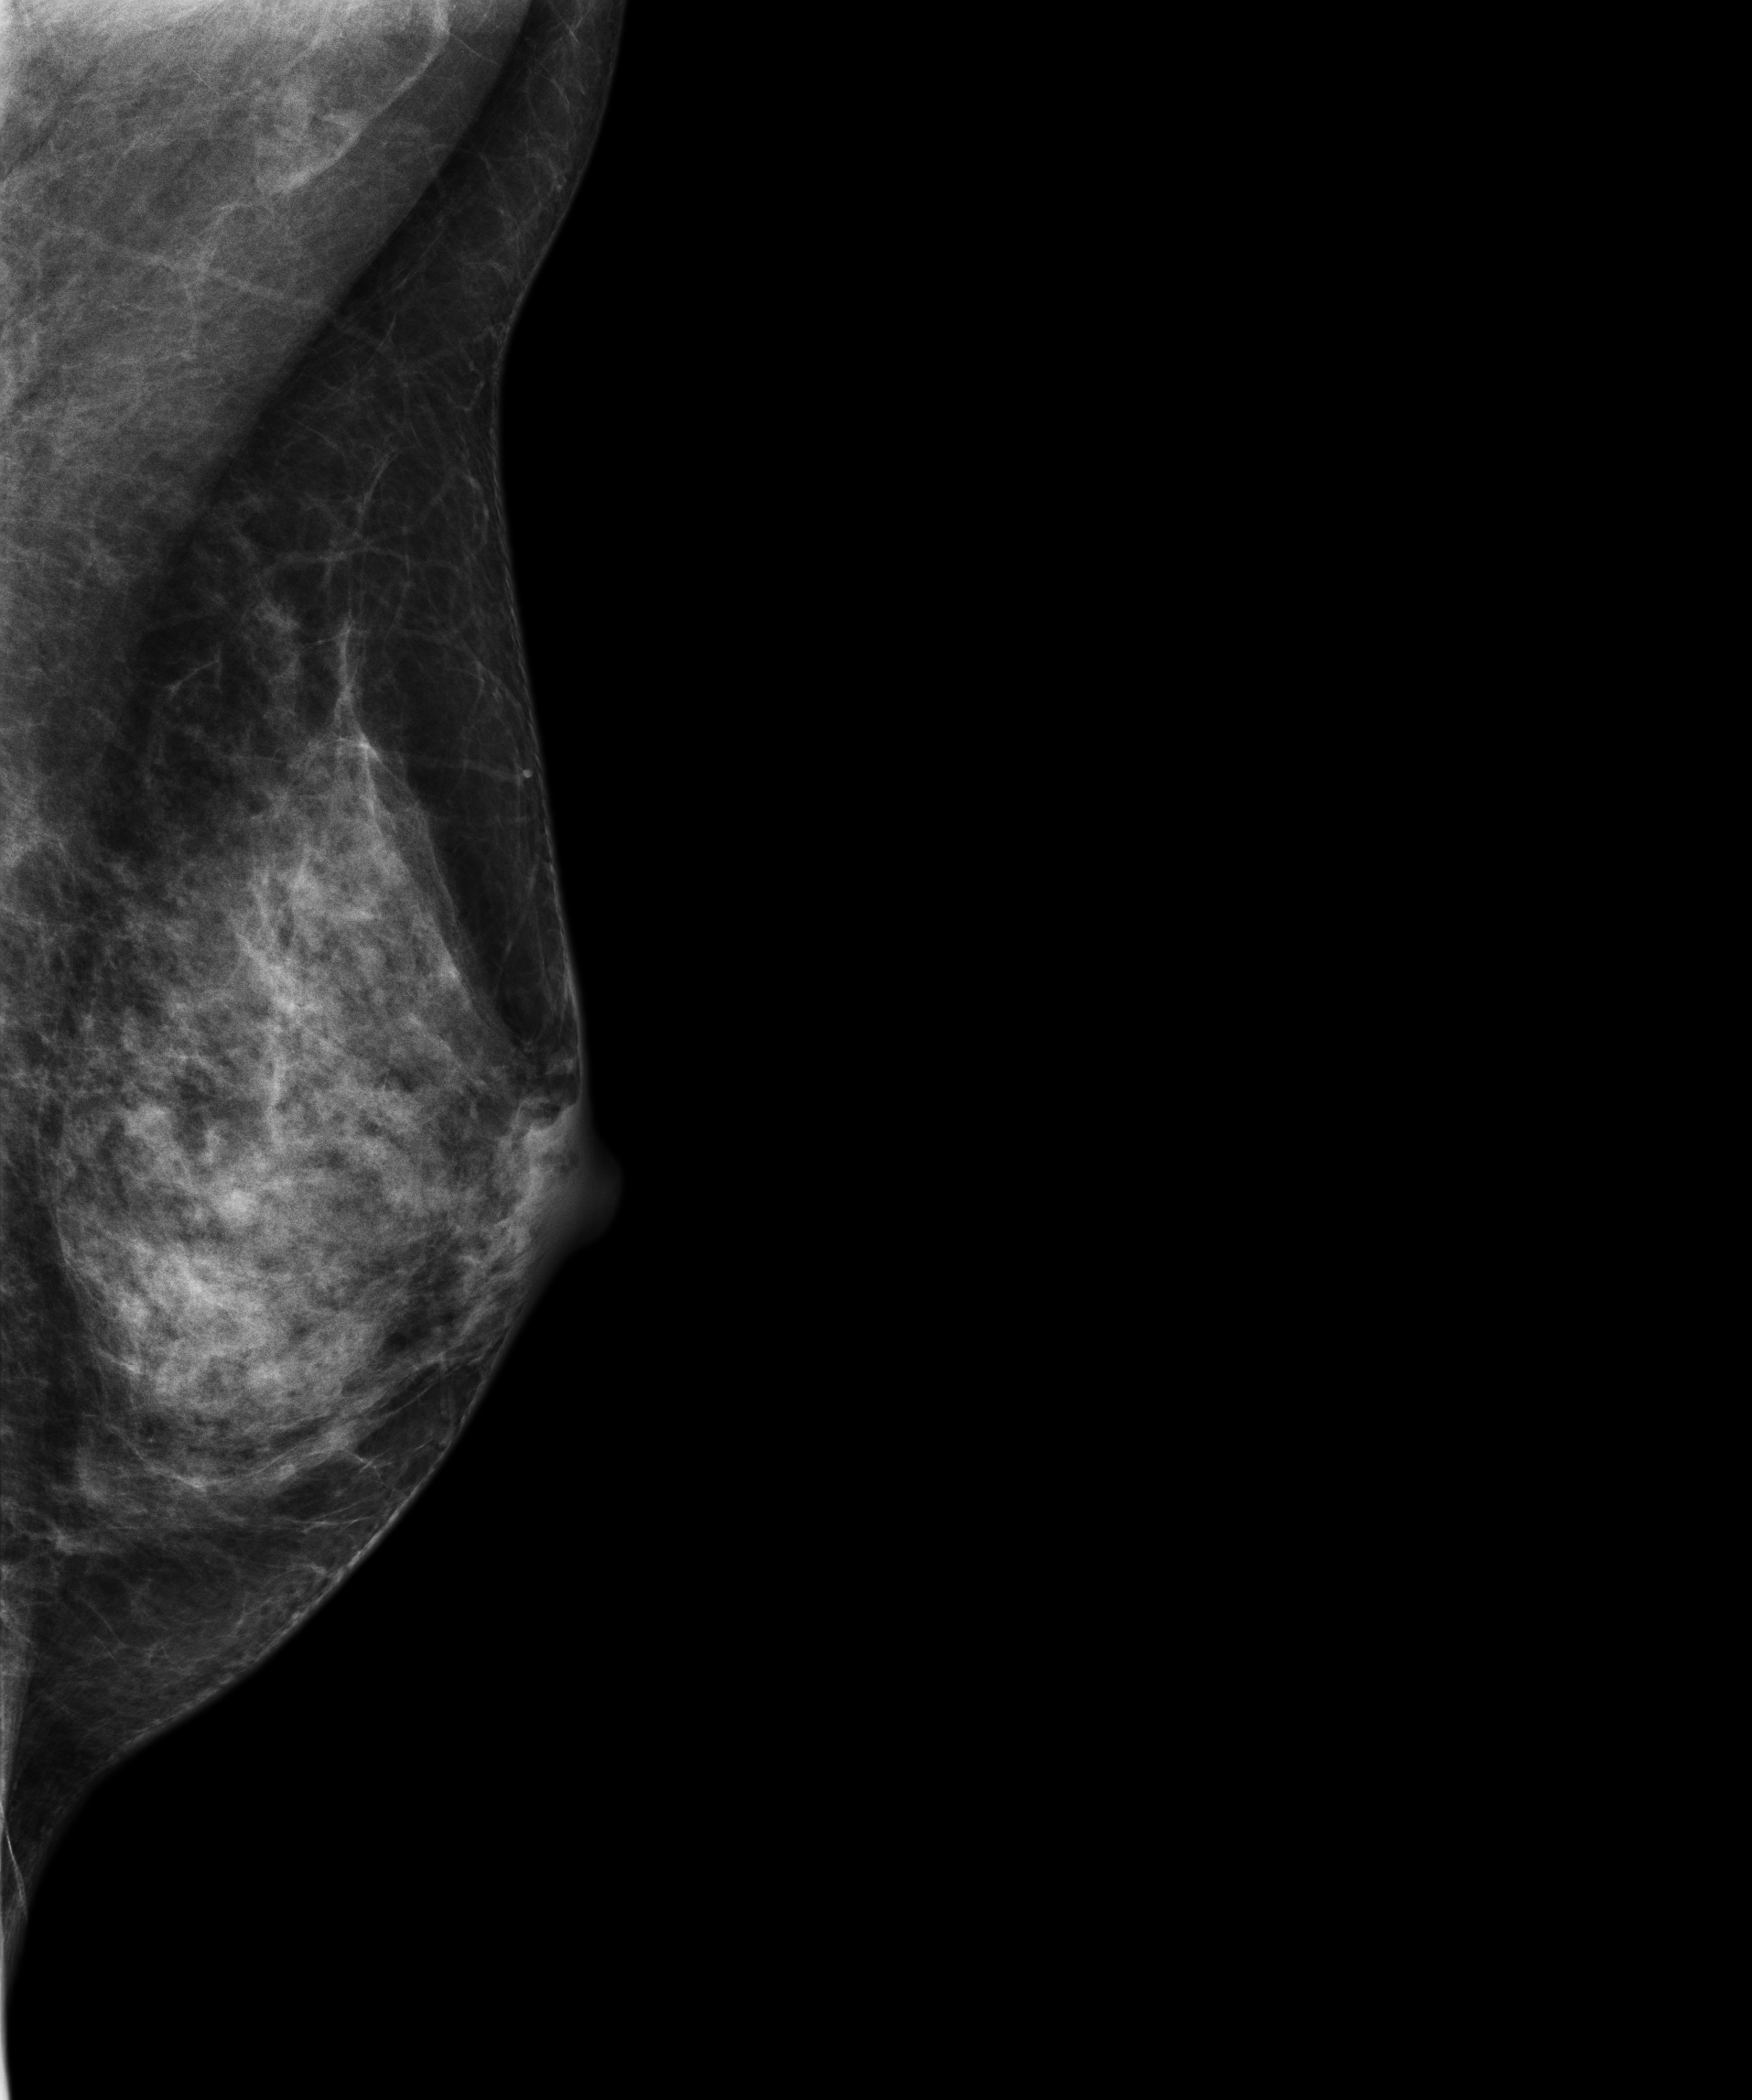
Annual screening mammography examination; compressed breast thickness 48 mm; system: Senographe Essential ADS_56.21.3. Patient: female, 56 years.
Image type: full-field digital mammogram. Breast: left. Projection: MLO view.